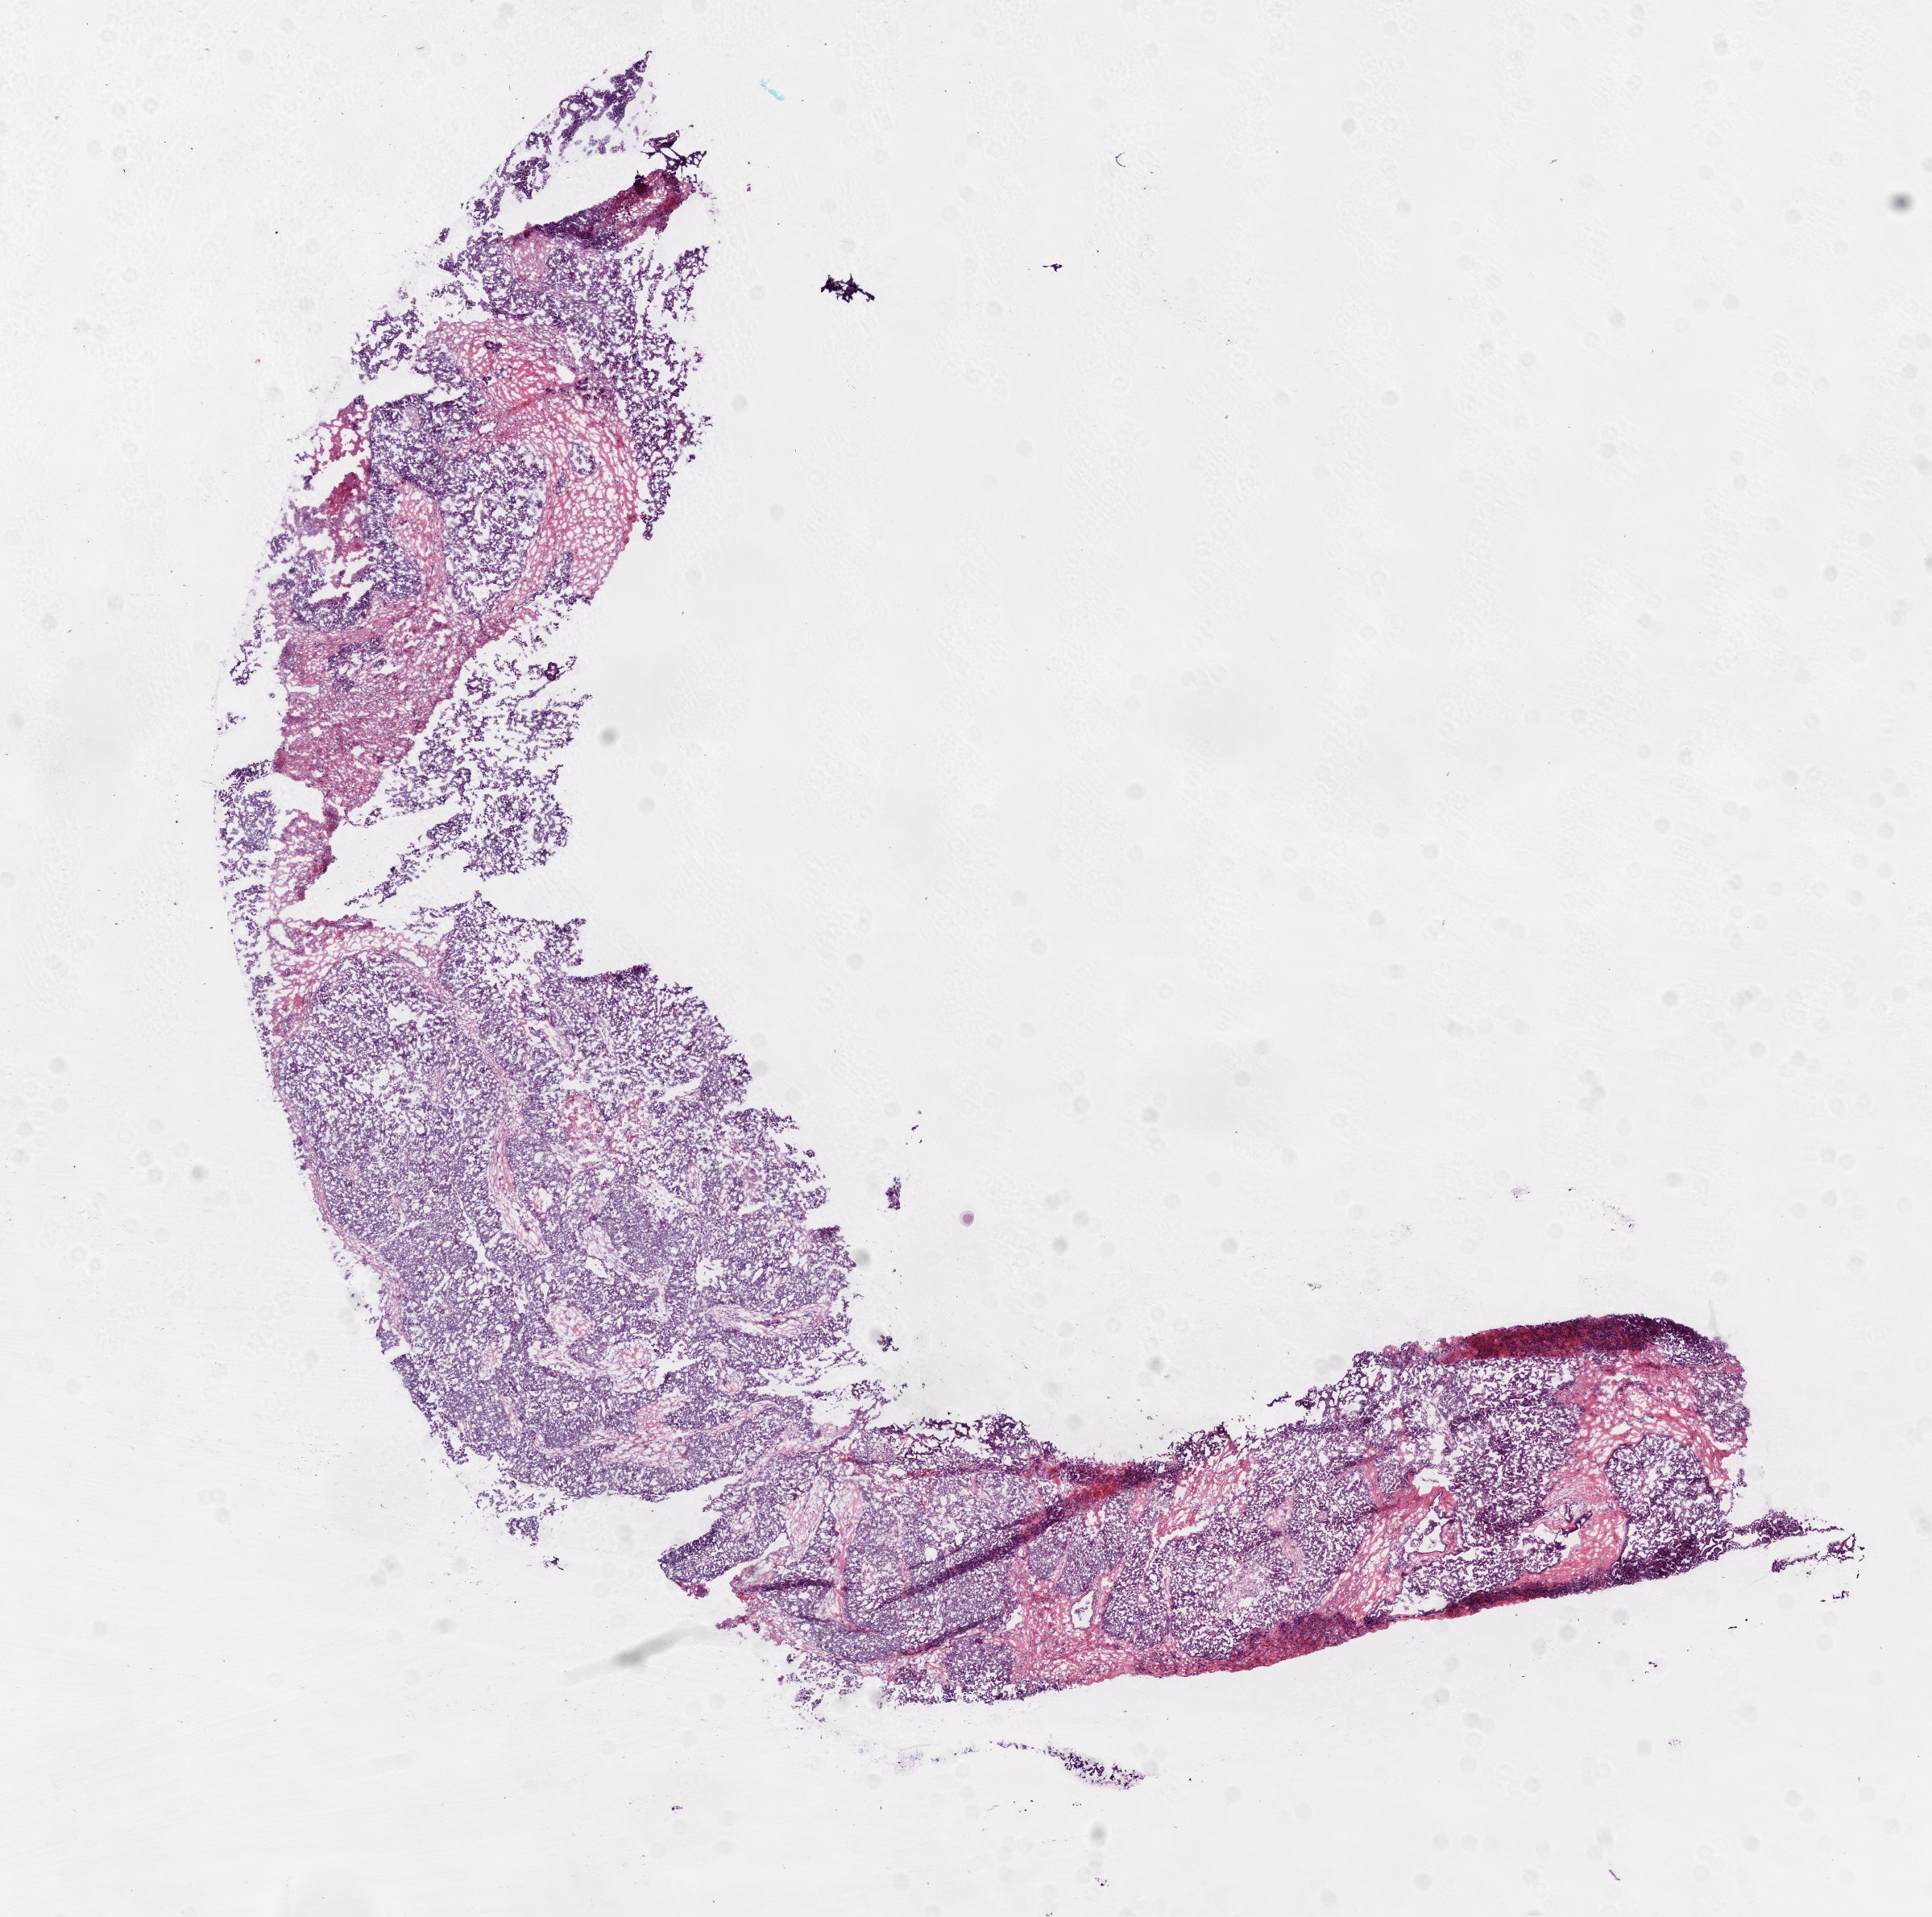
Digitized Hematoxylin and eosin (H&E) stained tissue section (whole slide) — shown as a low-resolution overview of the whole scanned area (about 9.7 x 9.6 mm, slide scanned at 20x), frozen section from the bottom of the tissue portion, primary tumour sample from the ovary. Patient: female, age at initial diagnosis 45 years. Histologic grade: G3 (poorly differentiated). Composition of this section per pathologist review: tumour nuclei 80%, normal cells 0%, stromal cells 0%, necrosis 5%.
Histologic diagnosis: Serous cystadenocarcinoma, NOS. FIGO stage: IV. Laterality: right.